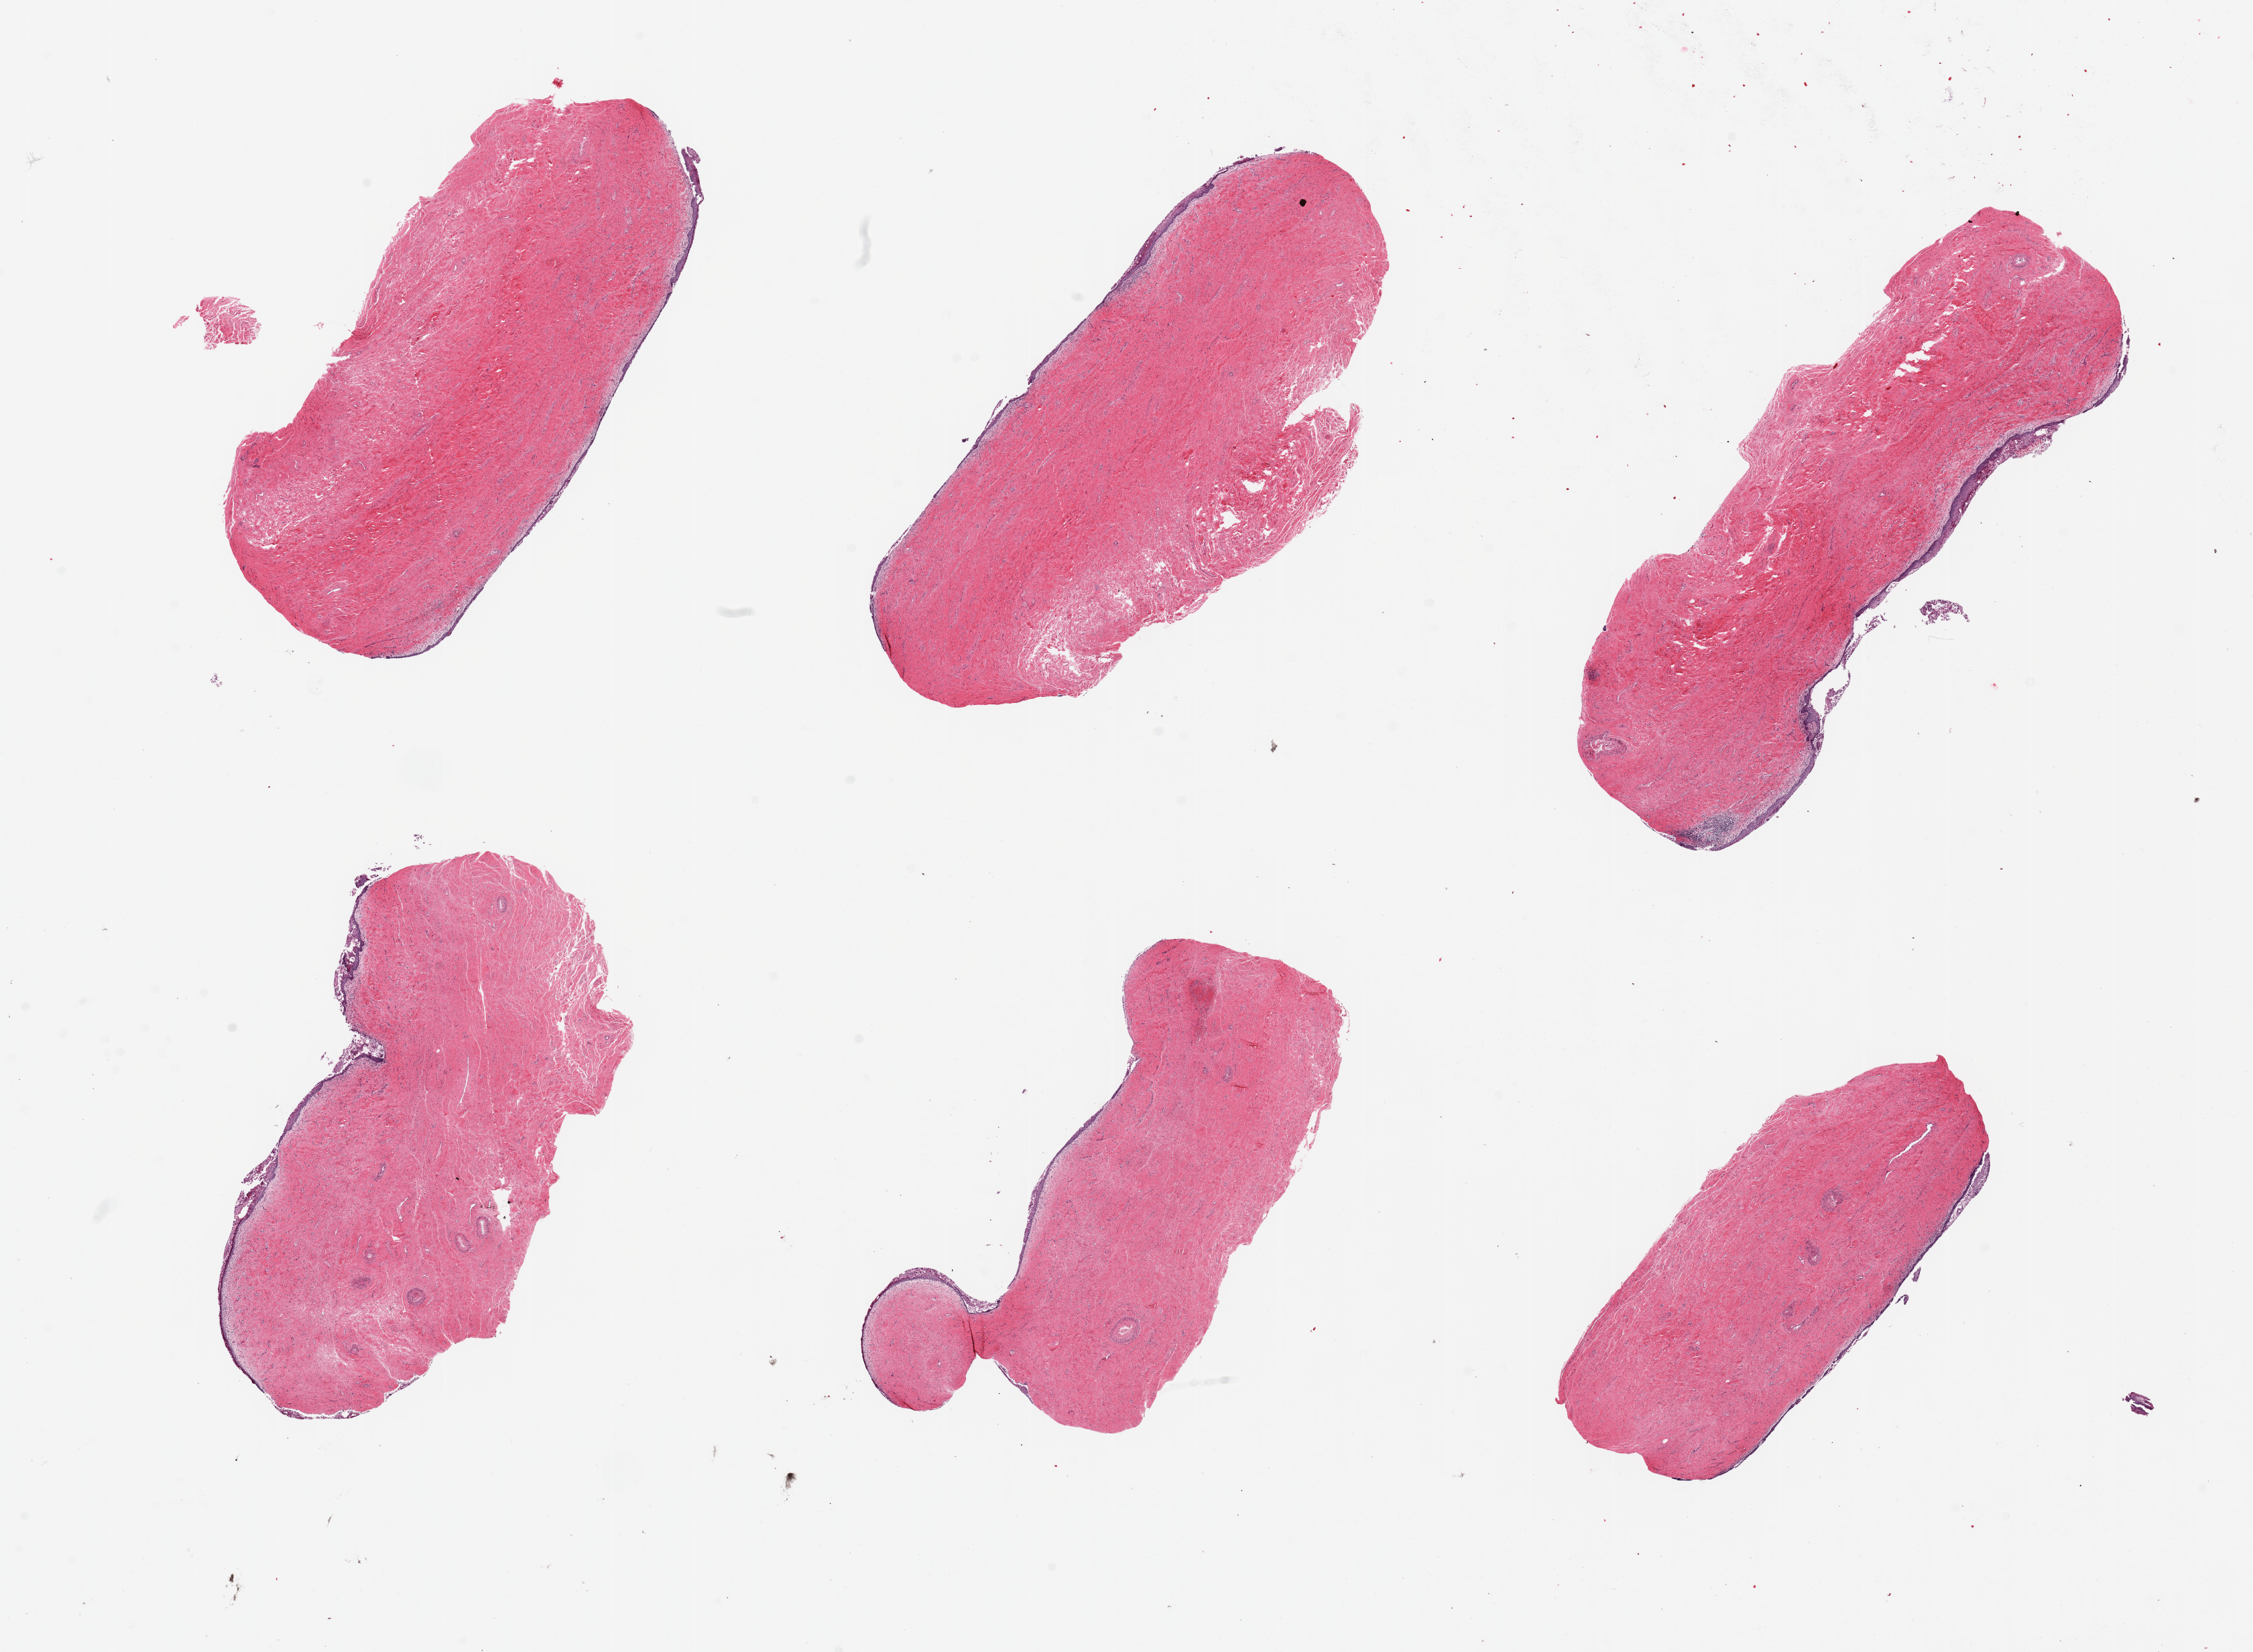
Whole-slide image, H&E stain, shown as a low-resolution overview of the whole scanned area (about 26.6 x 19.5 mm); PAXgene-fixed paraffin-embedded (PFPE) section; section of vagina (target tissue); tissue donor sample.
Review note (as recorded): 6 pieces; epithelium atrophic and largely sloughed.